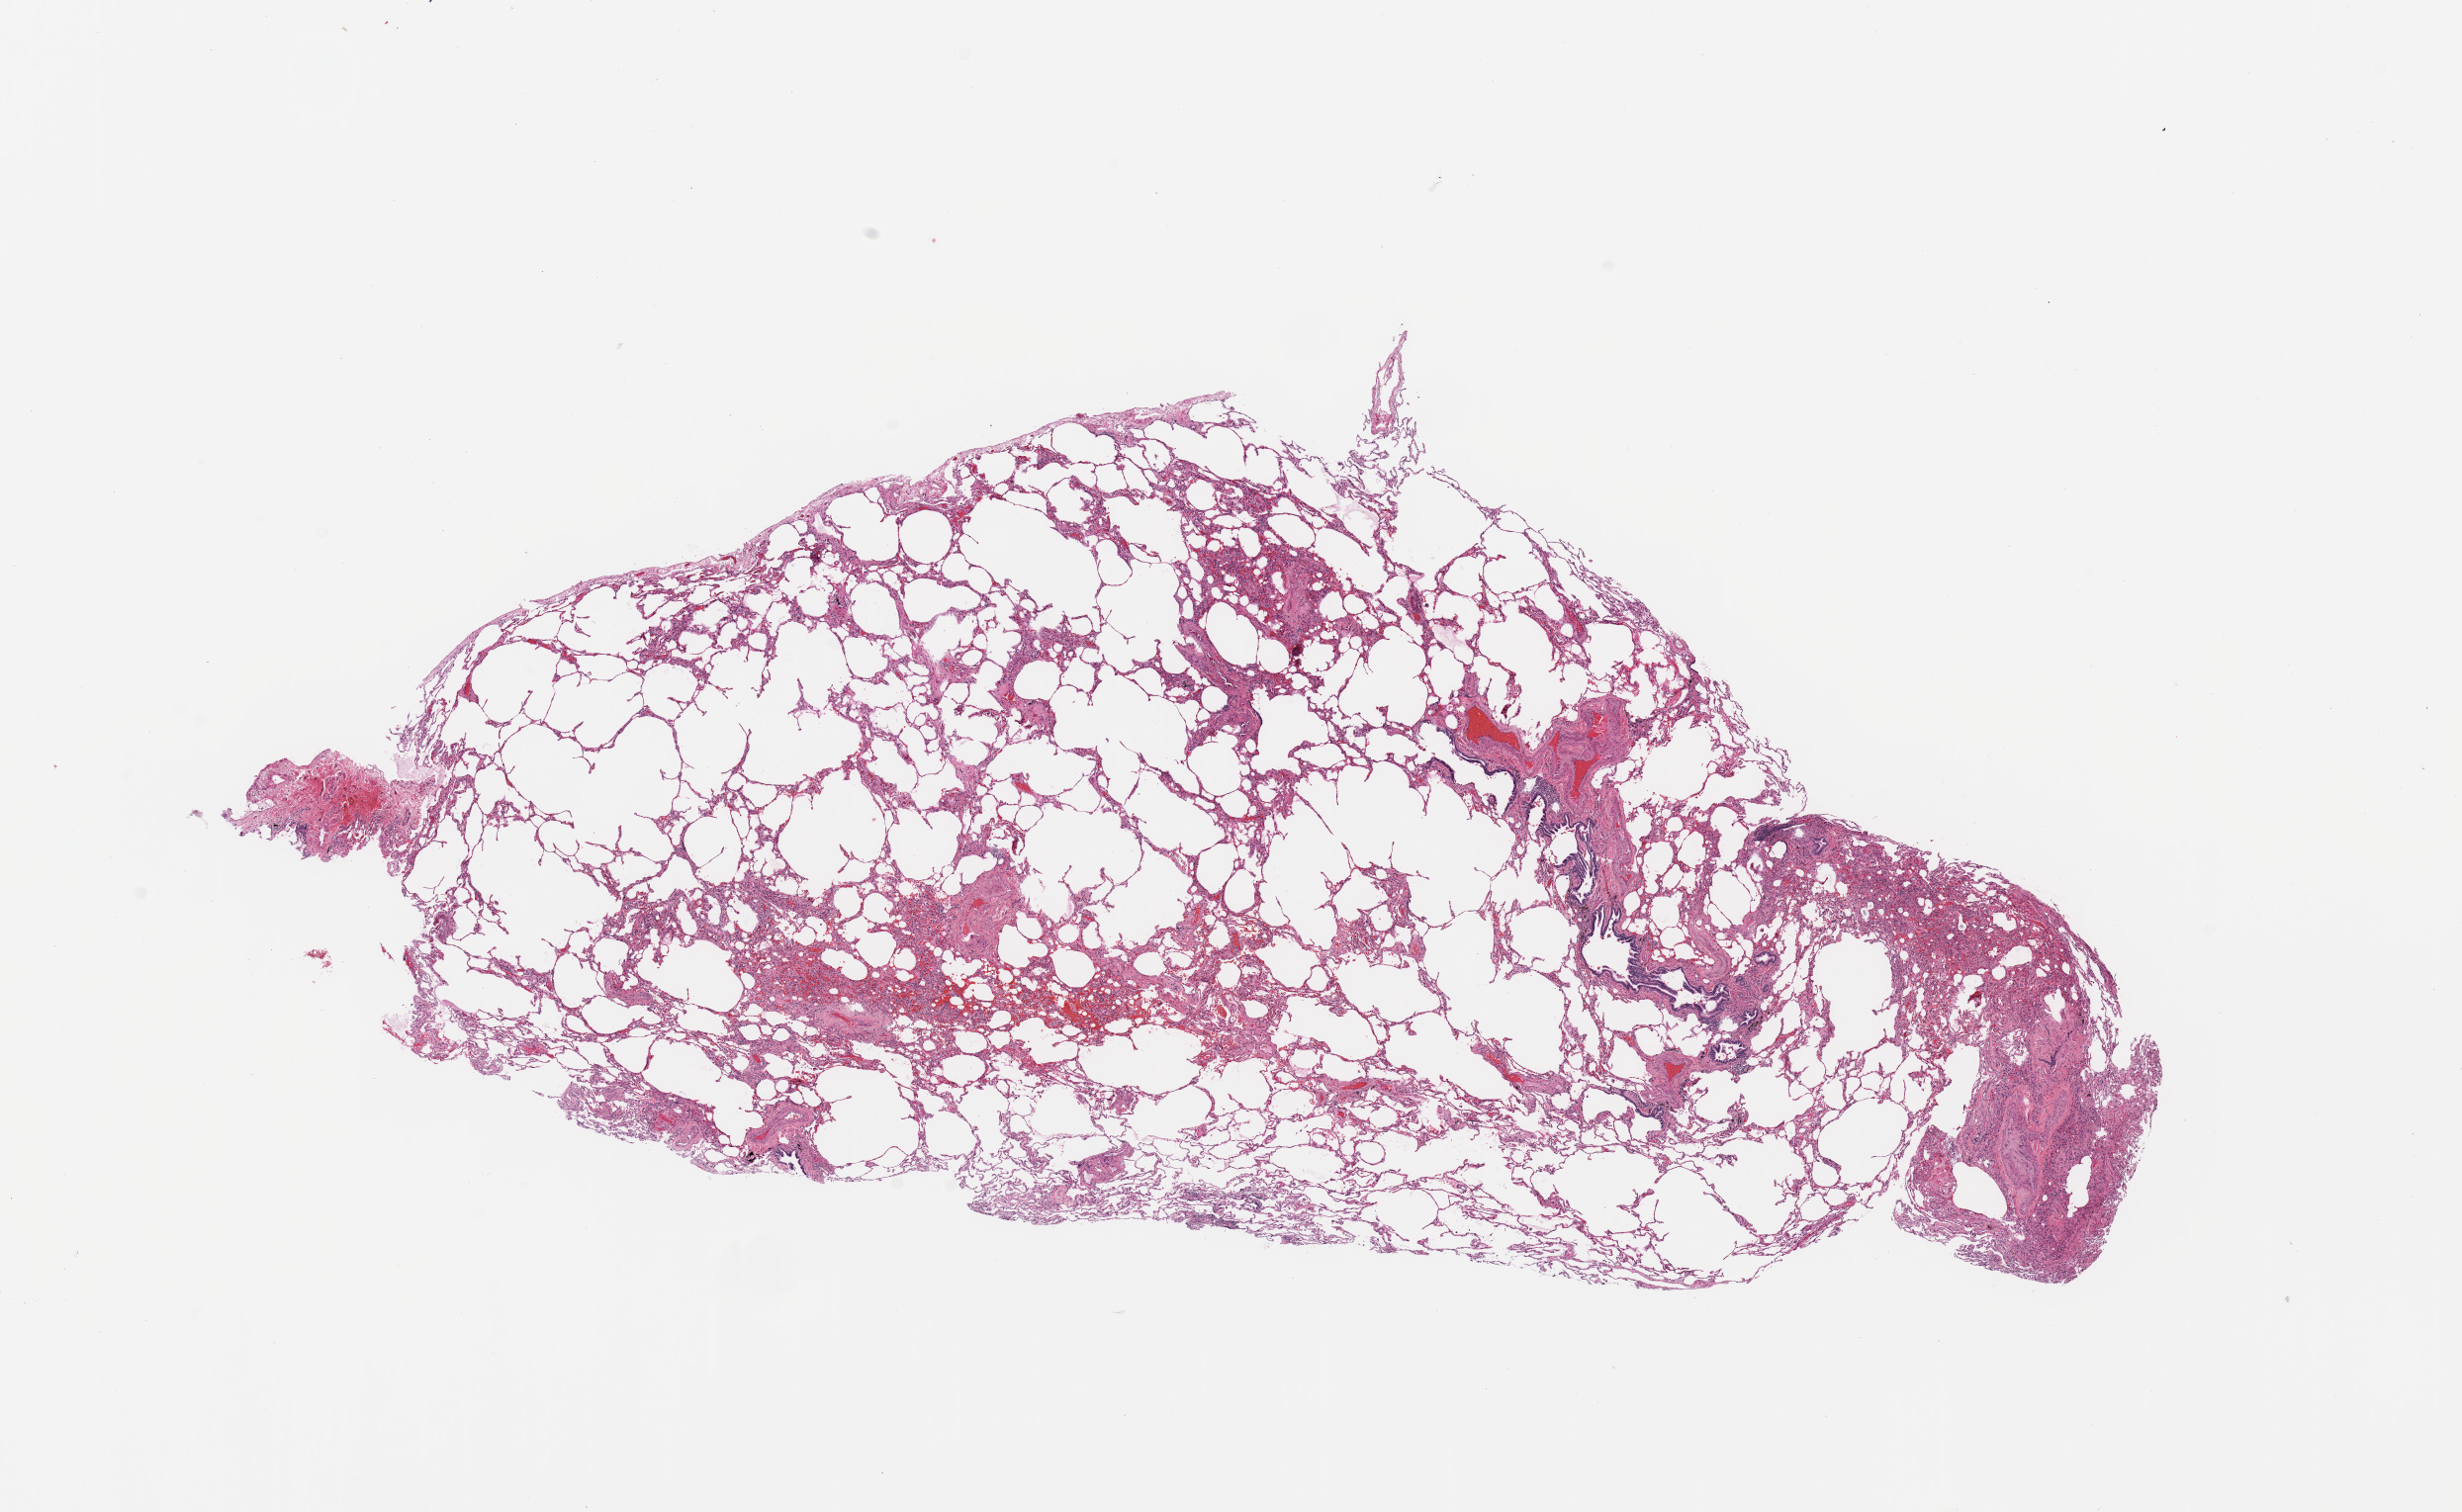
Hematoxylin and eosin (H&E) stained whole-slide image — a low-resolution overview of the entire scanned area, about 19.7 x 12.1 mm, normal (non-tumour) tissue sample, sampled site: lung. 76-year-old male patient.
This section: normal (non-tumour) tissue from the same patient. Patient diagnosis: Adenocarcinoma, NOS.